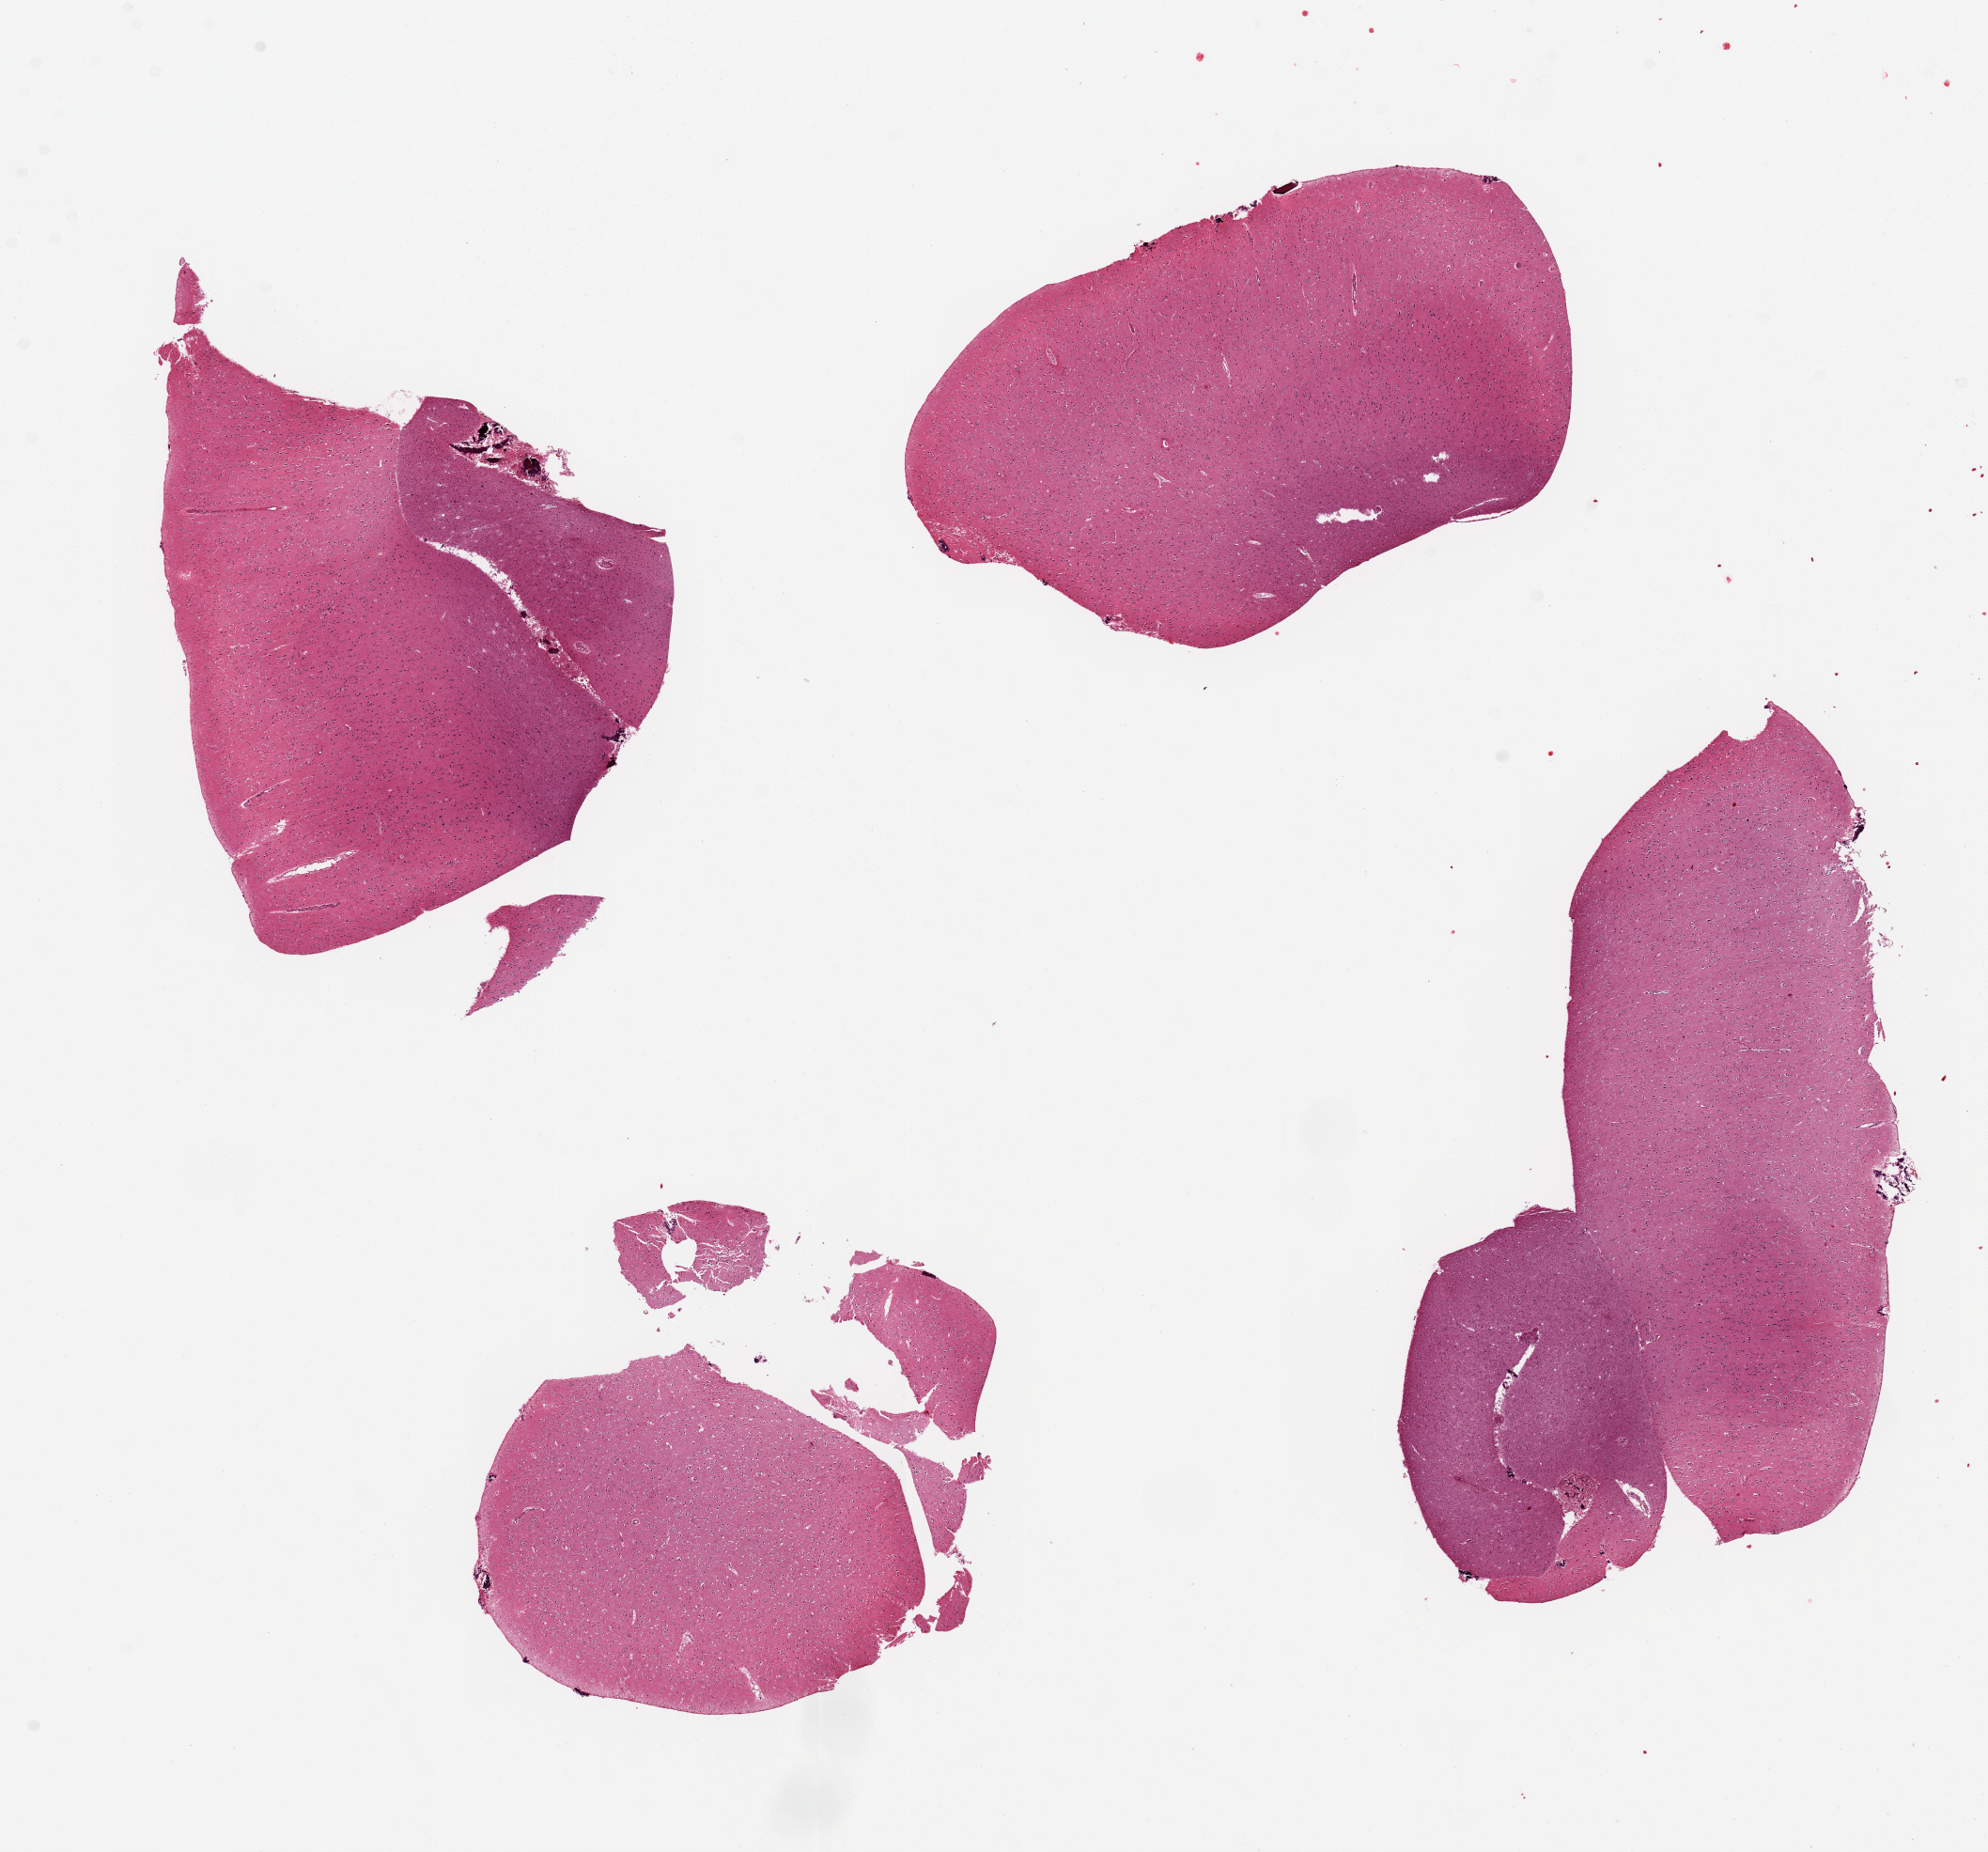
Digitized haematoxylin and eosin-stained section — shown as a low-resolution overview of the whole scanned area (about 16.7 x 15.6 mm); PAXgene-fixed, paraffin-embedded tissue; sampled site (target tissue): cerebral cortex; tissue donor sample.
- pathologist's review note for this sample: 4 fragmented aliquots, ~ 6x4mm